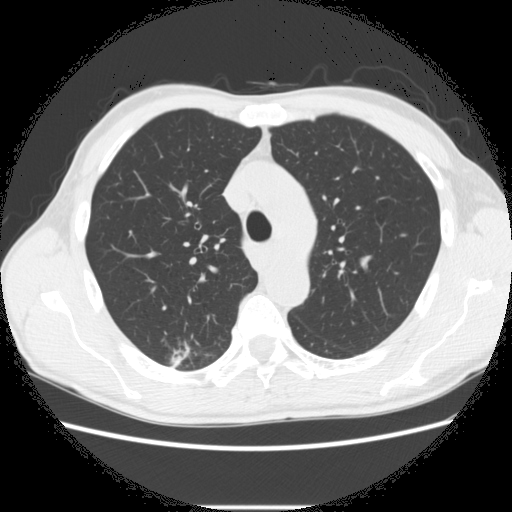
Low-dose screening chest CT, axial slice, second annual screen, lung window (W 1500 / L -600 HU), 2.5 mm slice thickness, slice 79 of 282 in the series. Male, age 66 years at enrolment. Former smoker at enrolment.
Expert reader's lesion annotation, box from (x=162, y=339) to (x=221, y=377) px. The screening reader recorded 5 non-calcified nodules or masses ≥4 mm on this exam (right lower lobe, right upper lobe, right upper lobe, right upper lobe, left lower lobe); which of them this box marks is not recorded. Later outcome: lung cancer diagnosed 75 days after this screen — adenocarcinoma, NOS, right upper lobe, undifferentiated (G4), stage IA (AJCC 6th edition), 20 mm at pathology.